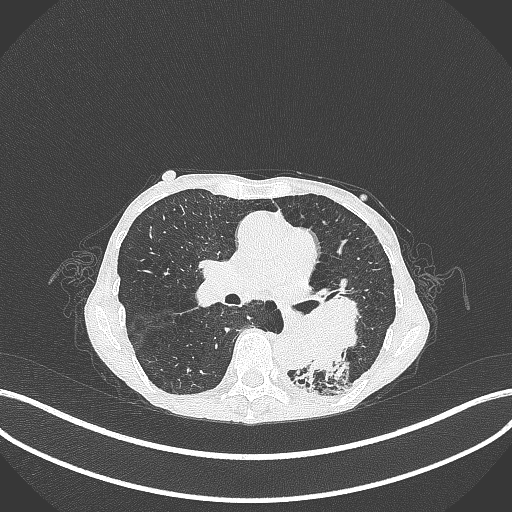
Chest CT, one axial slice; position 149 of 347 along the scan axis; 120 kVp; lung window (W 1500 / L -600 HU); 1 mm slice thickness; 512 × 512 image matrix, field of view 400 × 400 mm. Patient: female, 70 years. Case-level facts recorded for this patient, not image findings: clinical TNM (as recorded): T3 N0 M0.
Annotated regions visible in this slice (bounding box drawn by a radiologist):
- lung tumour (recorded histology: small cell carcinoma): box from (x=271, y=289) to (x=370, y=375) px